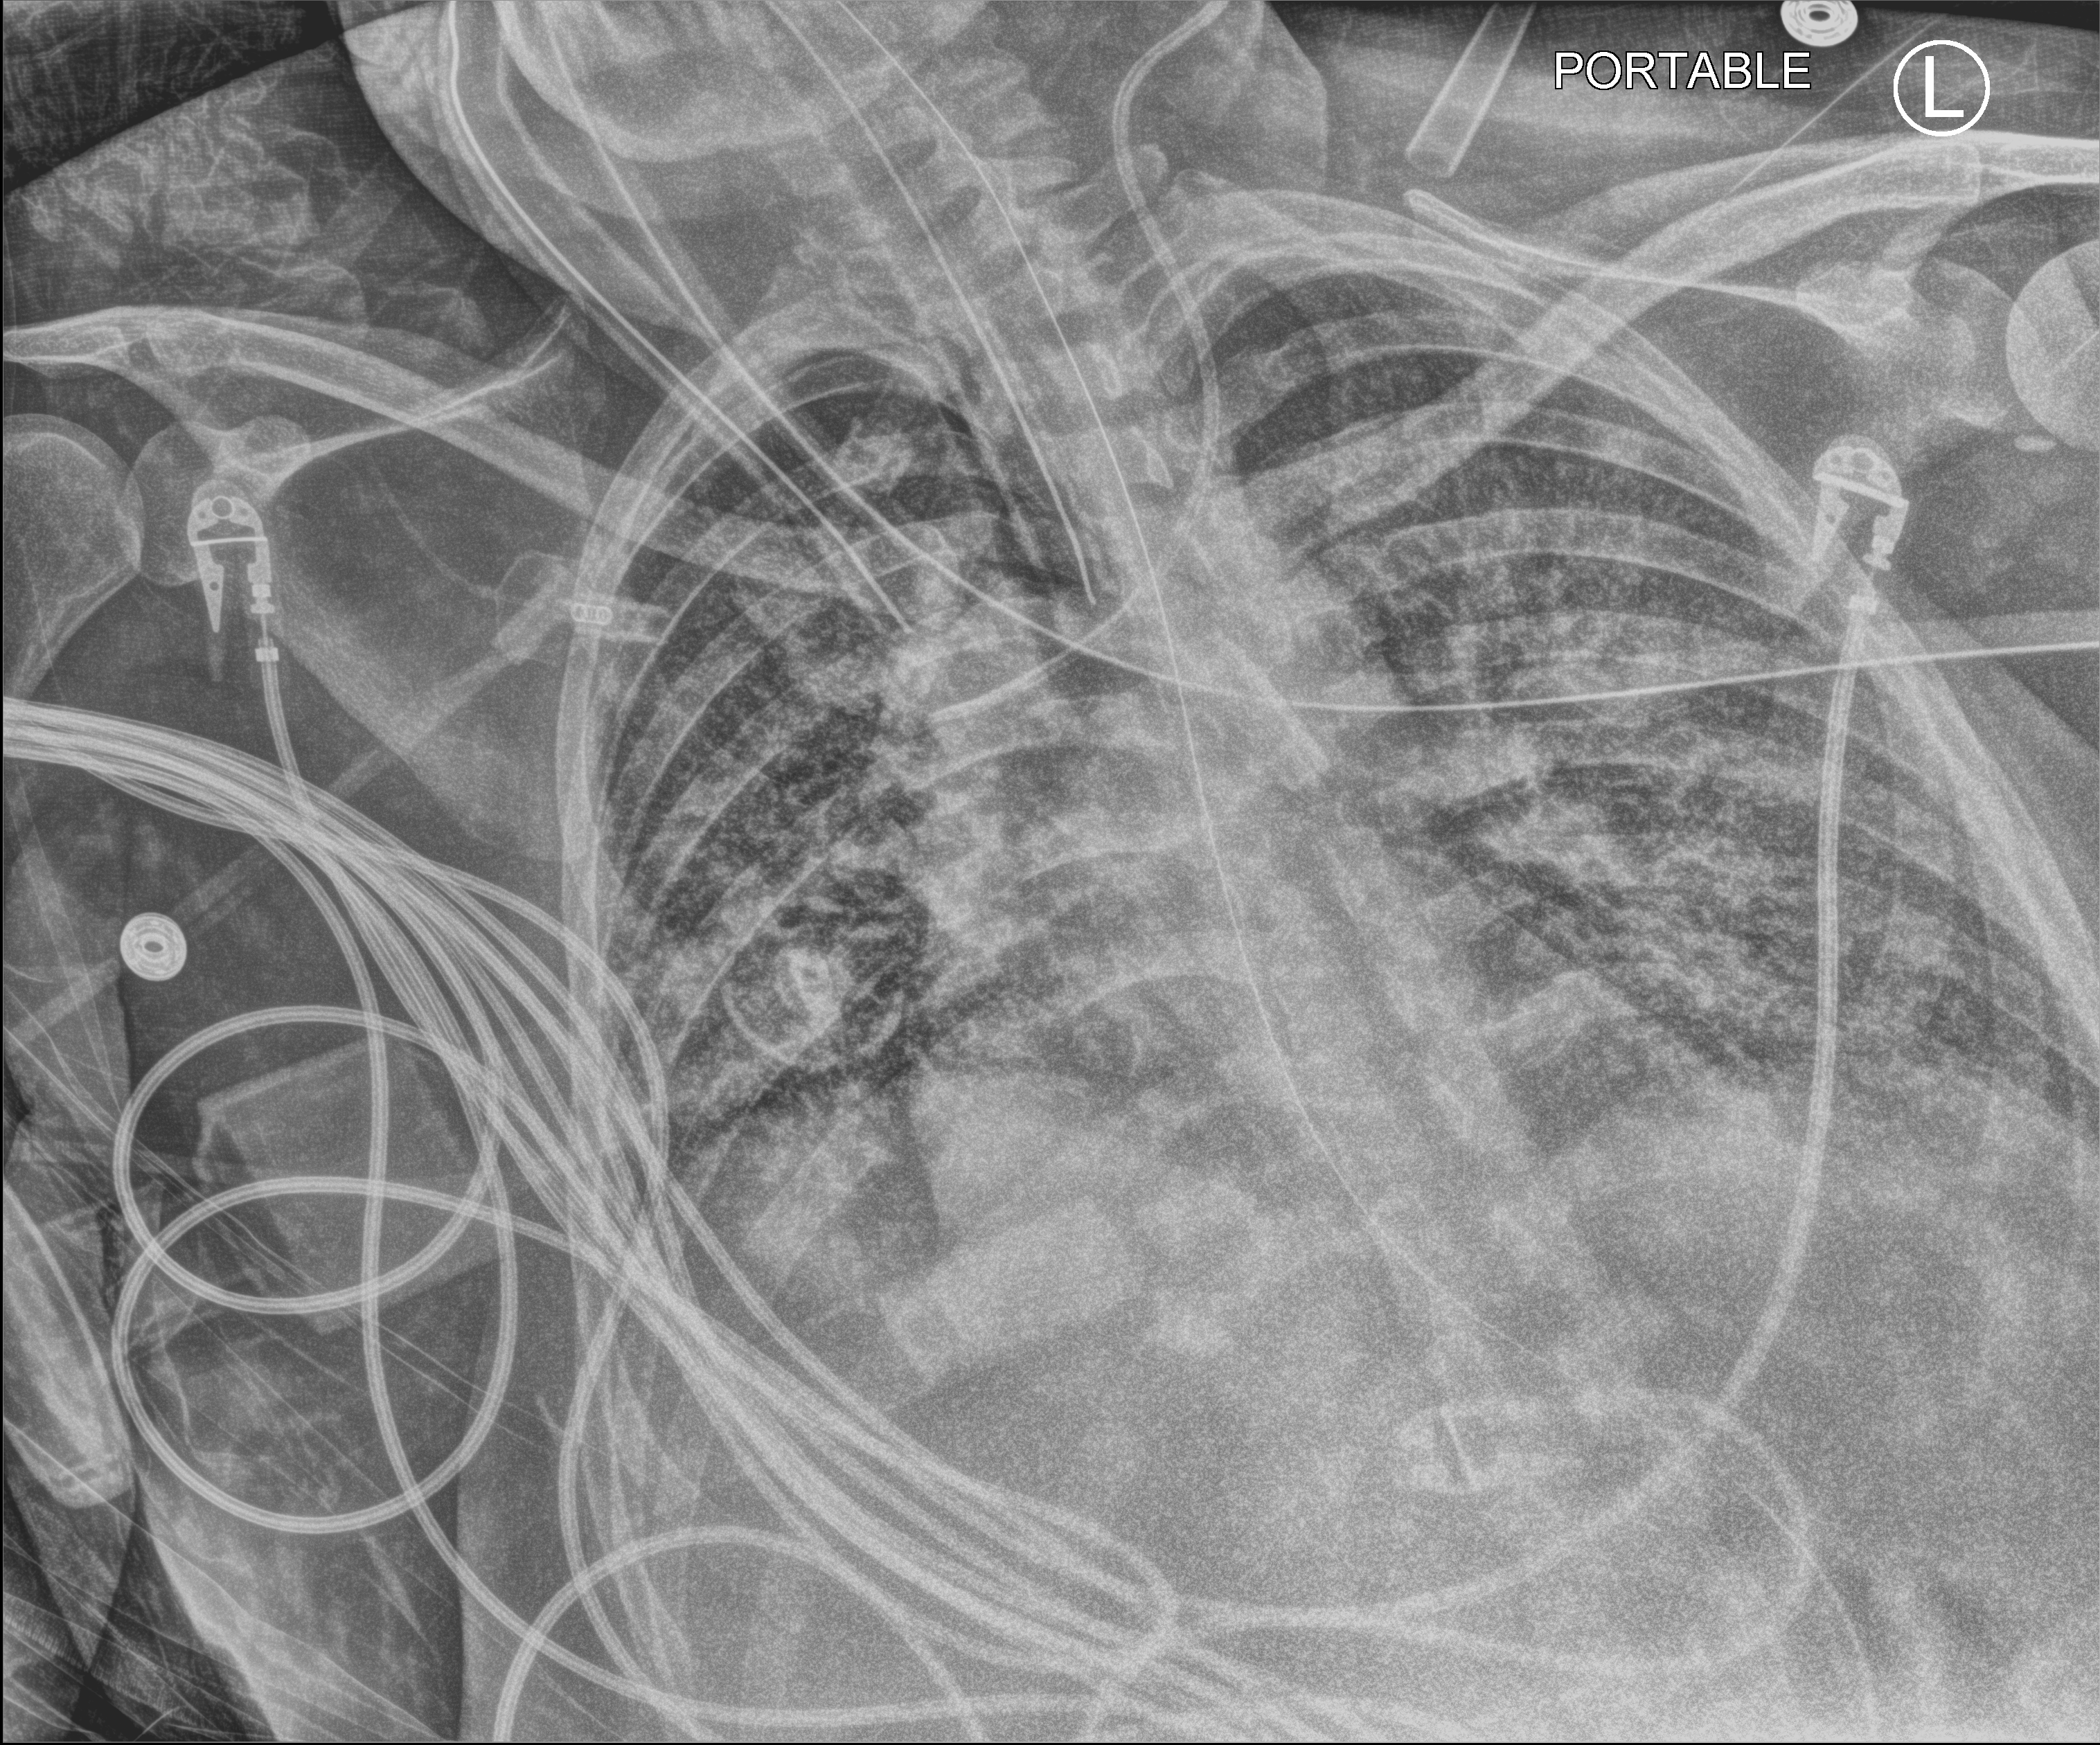
Portable chest radiograph, anteroposterior (AP) projection. Patient hospitalised with COVID-19; female, aged 18–59 years.
Hospital-stay facts (about this admission, not read from this image; timing relative to this image not recorded):
- mechanically ventilated during this hospital stay: yes
- admitted to intensive care during this hospital stay: no